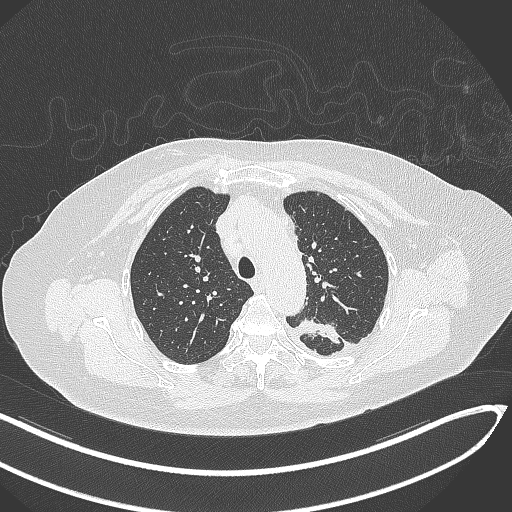
Chest CT, one axial slice; position 235 of 270 along the scan axis; reconstruction kernel B70f; lung window (W 1500 / L -600 HU); 1 mm slice thickness; 512 × 512 image matrix. Patient: female, 76 years. From the clinical record (not read from this slice): clinical TNM (as recorded): T1c N0 M0.
Annotated regions visible in this slice (bounding box drawn by a radiologist):
- lung tumour (recorded histology: adenocarcinoma): bounding box [x1, y1, x2, y2] px = [294, 319, 342, 346]